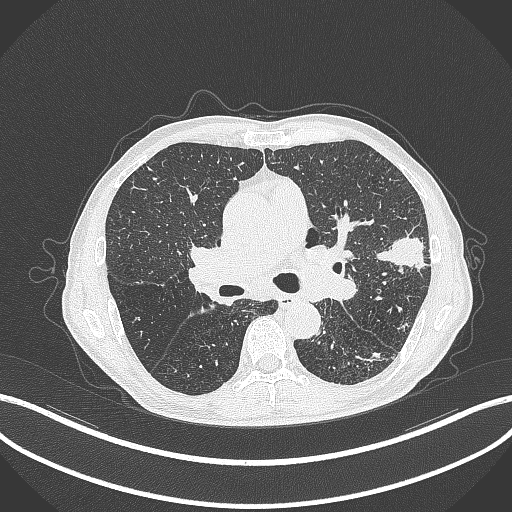
Chest CT, one axial slice. Slice 248 of 463 in the series (ordered by position). Reconstruction kernel B70f. 120 kVp. Lung window (W 1500 / L -600 HU). 1 mm slice thickness. 512 × 512 image matrix, field of view 400 × 400 mm. Patient: male, 74 years. Case-level facts recorded for this patient, not image findings: clinical TNM (as recorded): T2a N1 M0.
Structures marked on this image (rectangle marked by the reading radiologist):
- lung tumour (recorded histology: adenocarcinoma): box from (x=373, y=236) to (x=428, y=272) px